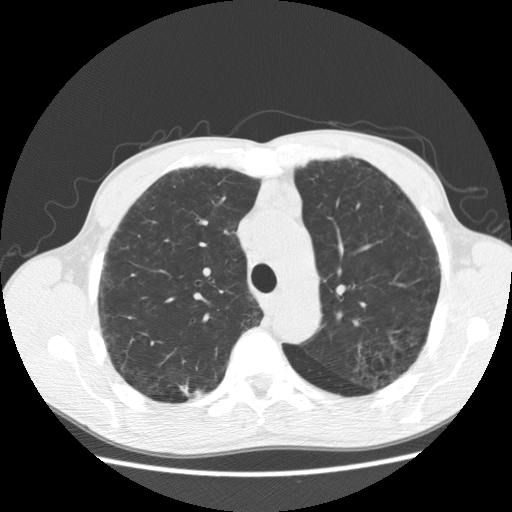
Low-dose screening chest CT, one axial slice; slice 139 of 195 in the series (ordered by position); reconstruction kernel STANDARD; lung window (W 1500 / L -600 HU); 512 × 512 image matrix.
Annotated regions visible in this slice (manually delineated by an expert):
- lesion 1 (tumor, upper lobe of right lung): bounding box (x1, y1, x2, y2) in pixels: (181, 385, 203, 397)